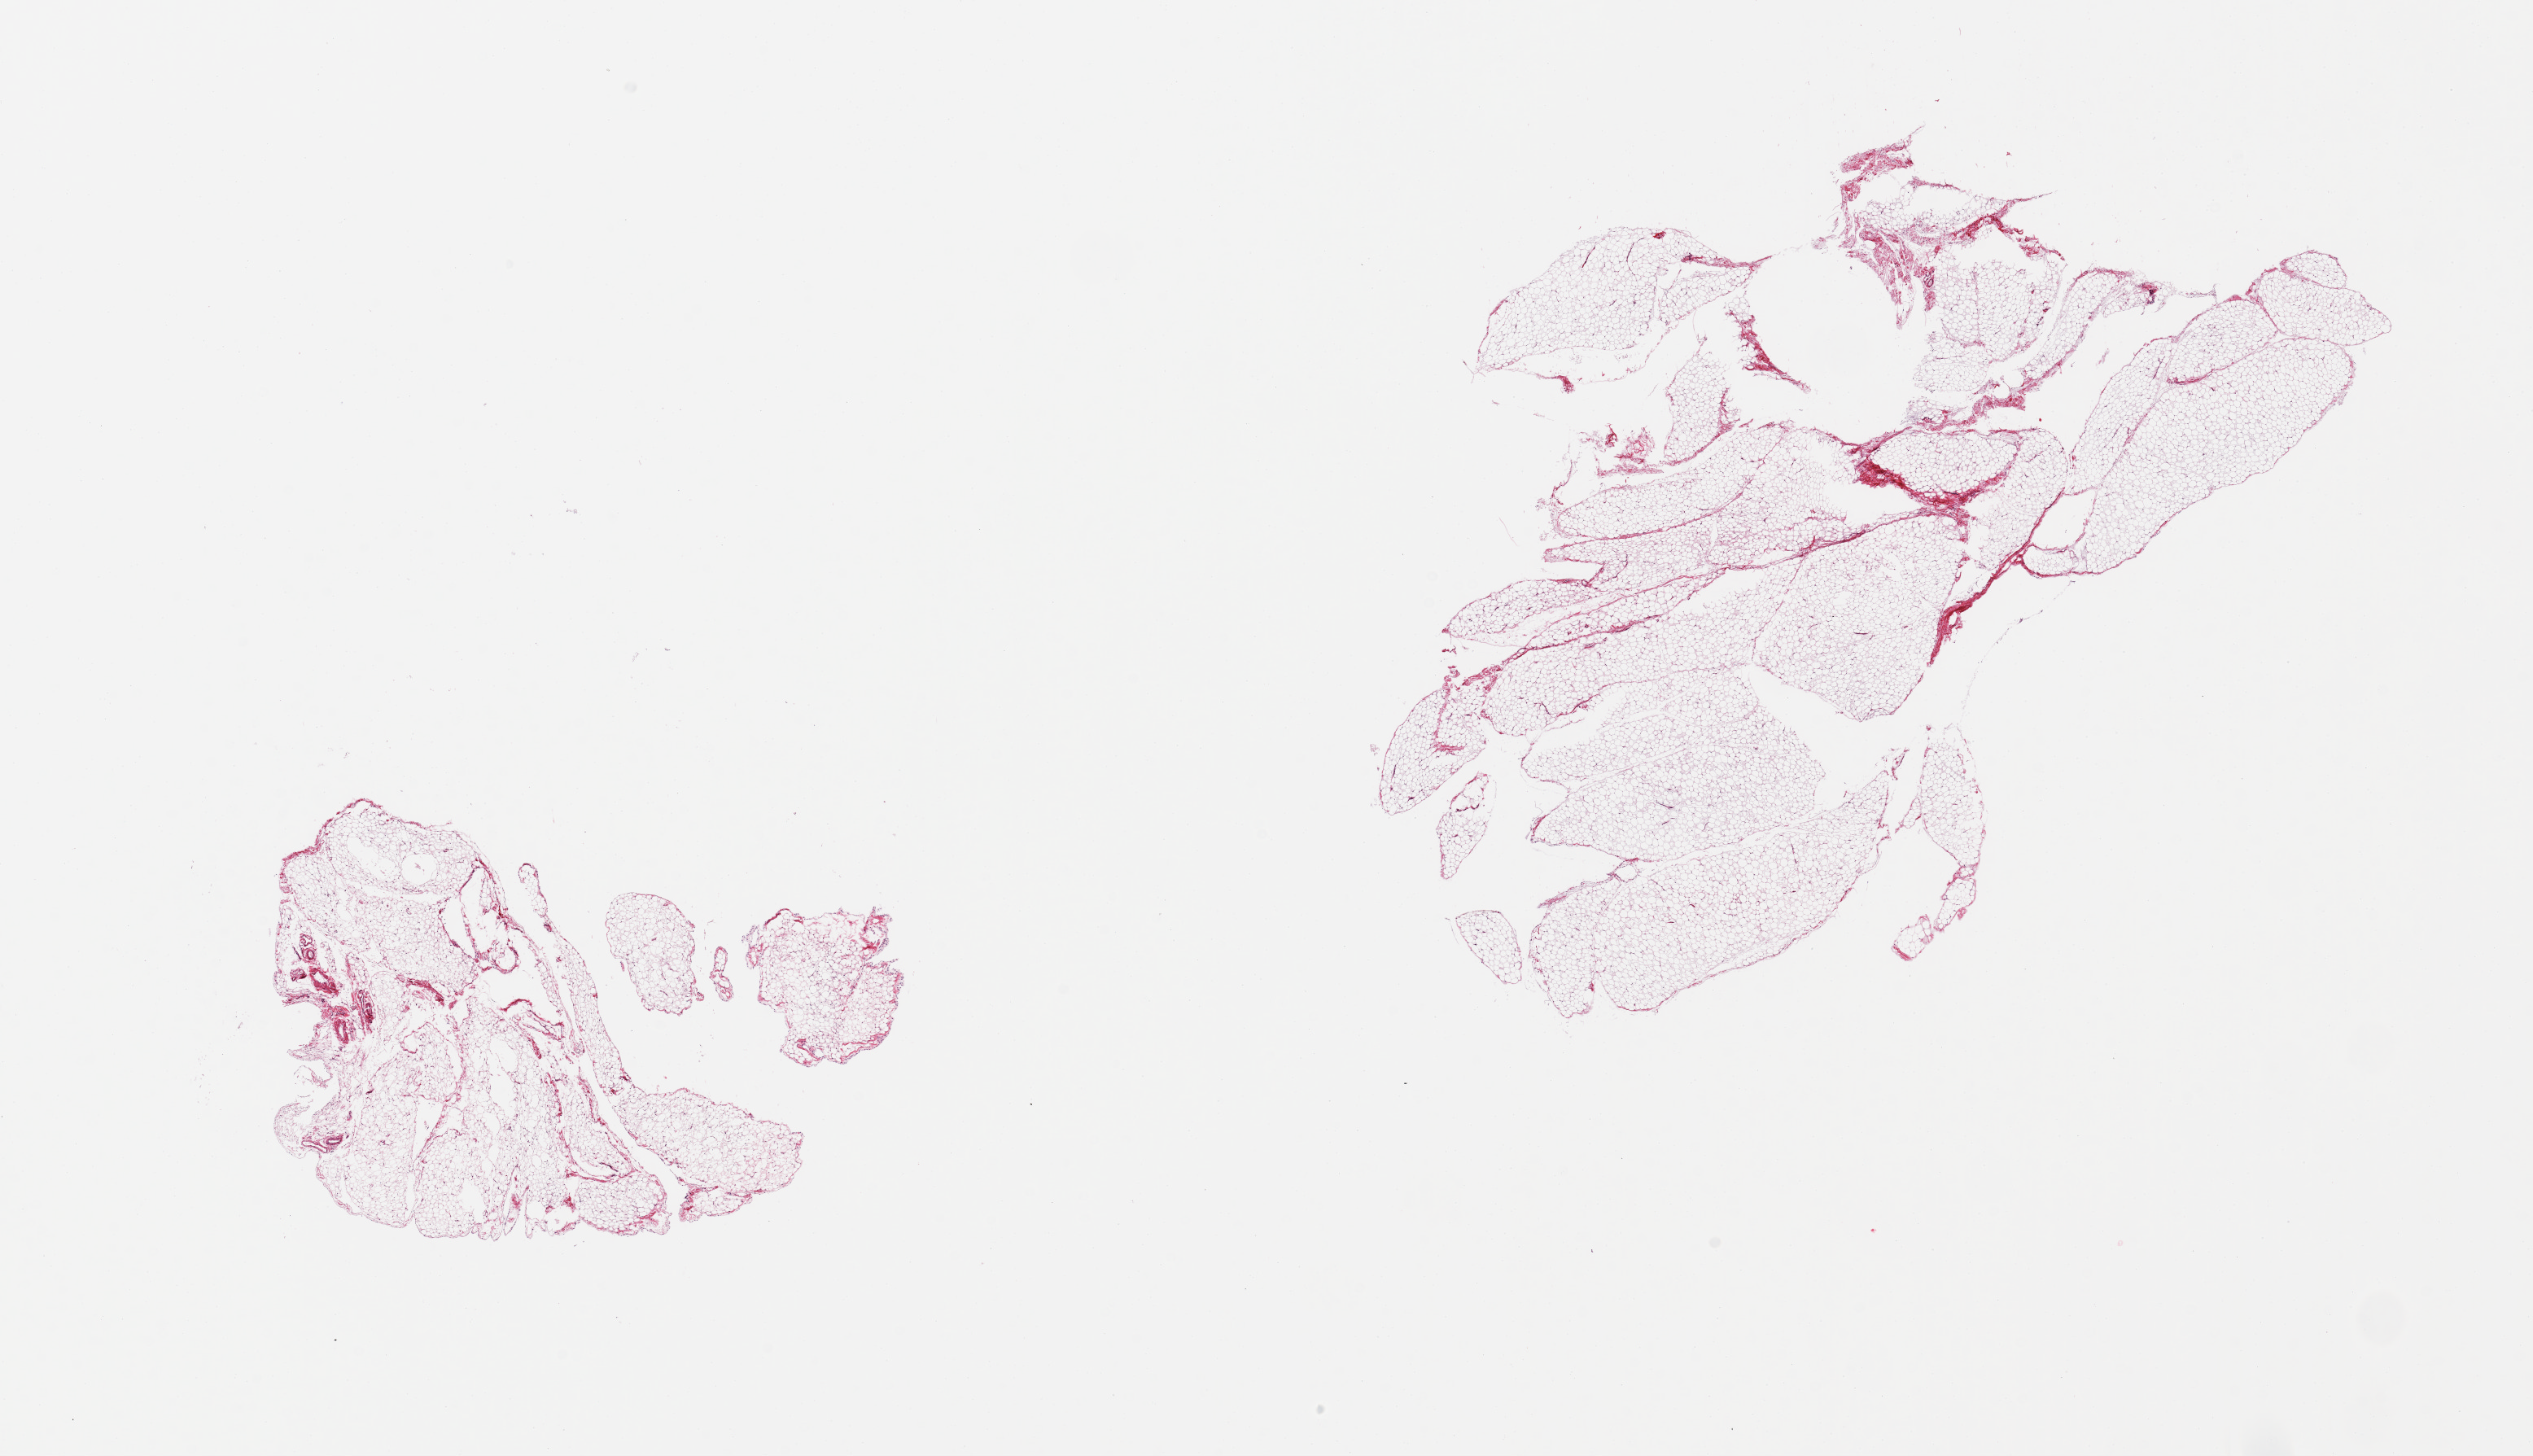
Digitized H&E-stained section — a low-resolution overview of the entire scanned area, about 24.6 x 14.1 mm (acquisition: 20x scan). PAXgene-fixed, paraffin-embedded tissue. Target tissue: omentum. Donor tissue sample. Male donor.
Pathologist's review note for this sample: 2 pieces; <5% fibrous content.